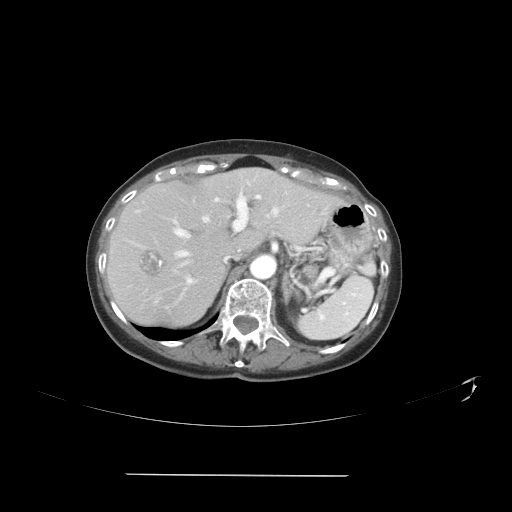
Contrast-enhanced abdominal CT, one axial slice. Position 27 of 41 along the scan axis. Intravenous contrast given. Soft-tissue window (W 400 / L 40 HU). 5 mm slice thickness. 512 × 512 image matrix, field of view 431 × 431 mm. Female patient, age 74 years. Case-level facts recorded for this patient, not image findings: diagnosis: colorectal cancer liver metastases, imaged before liver resection; multiple liver metastases: yes; largest metastasis: 3.3 cm; disease in both lobes: yes.
Outlined on this slice (expert manual segmentation):
- hepatic veins: box from (x=175, y=206) to (x=278, y=265) px
- liver: (x=106, y=168)–(x=333, y=329)
- planned liver remnant (the part of the liver to remain after resection): (x=115, y=168)–(x=309, y=258)
- portal vein (with intrahepatic branches): (x=174, y=193)–(x=261, y=283)
- liver metastasis: (x=318, y=203)–(x=328, y=214)
- liver metastasis: (x=140, y=250)–(x=163, y=276)